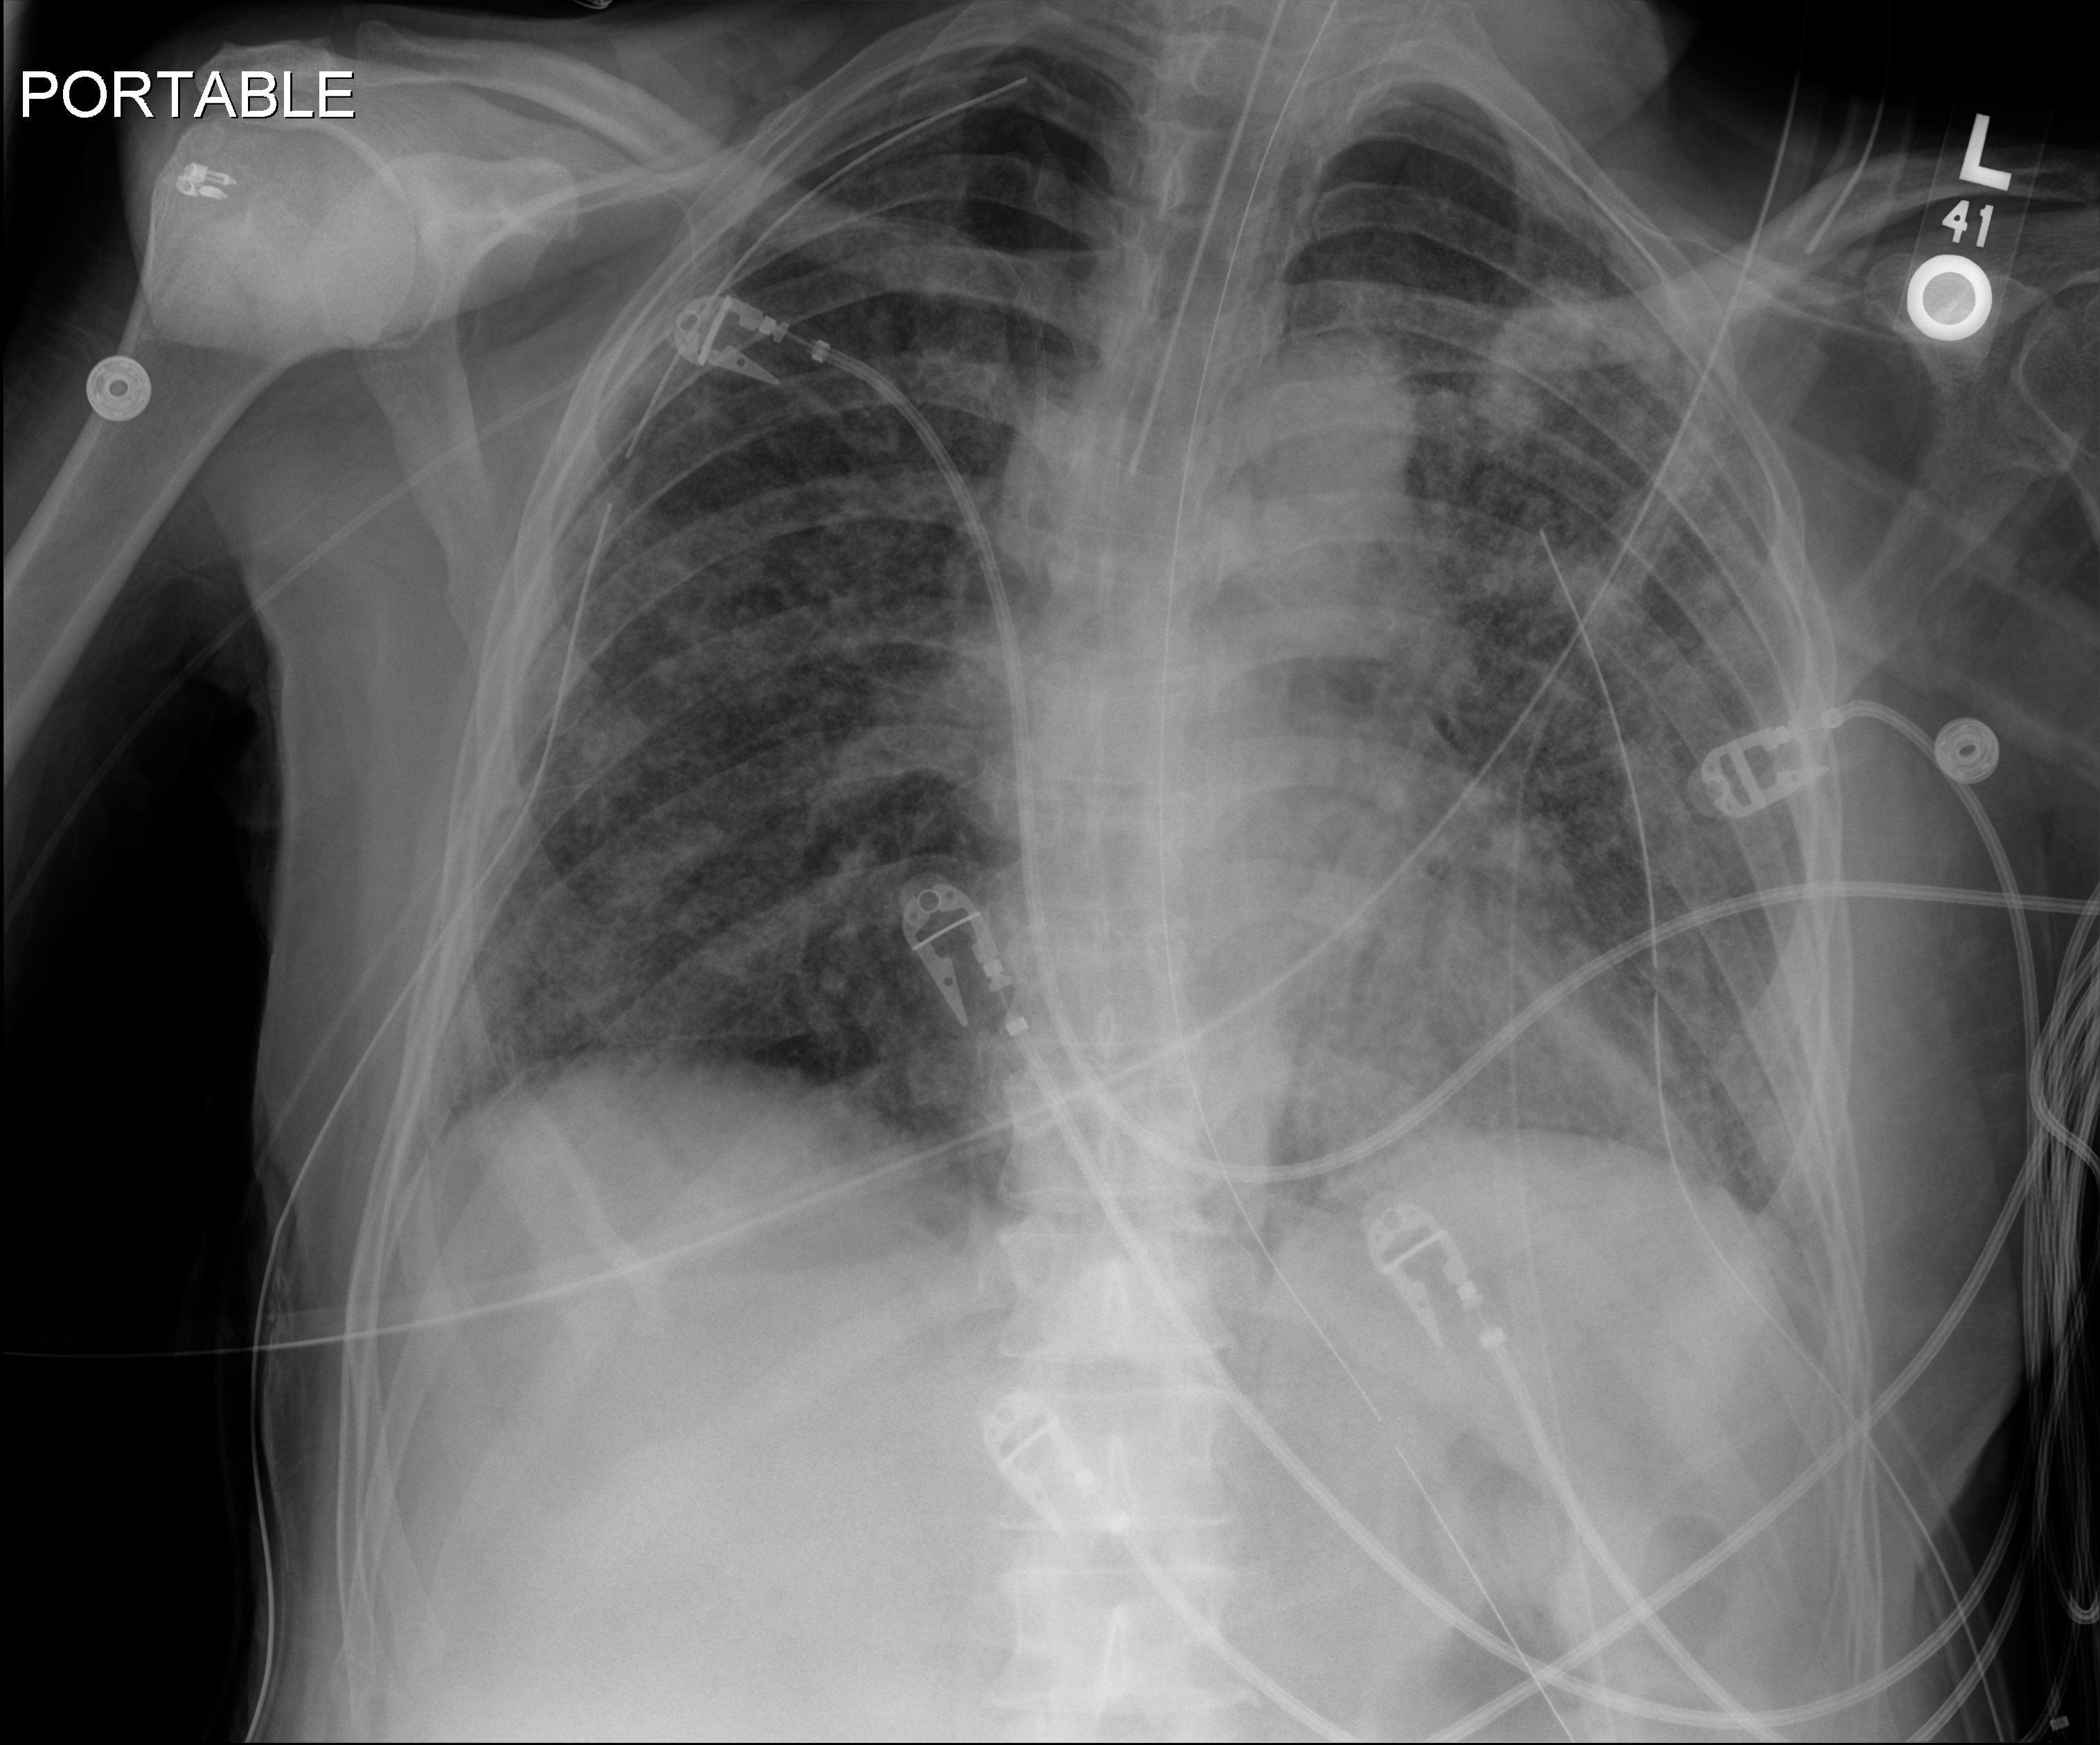
Bedside chest radiograph (digital radiography), anteroposterior (AP) projection. Patient hospitalised with COVID-19; male, aged 60–74 years.
From the hospital-stay record, not from the radiograph (when in the stay this image was taken is not recorded): mechanically ventilated during this hospital stay: yes; admitted to intensive care during this hospital stay: yes.